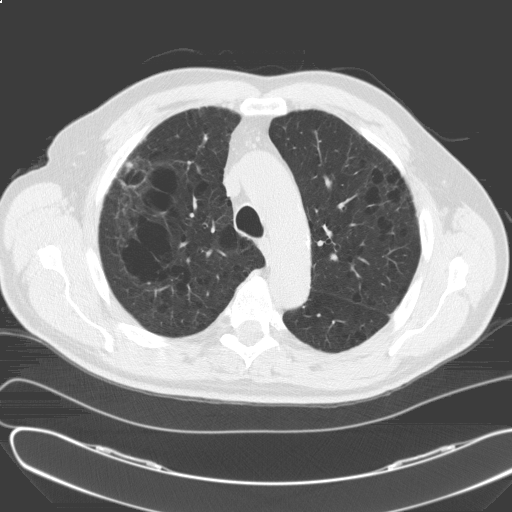
Chest CT (low-dose screening protocol), one axial image. Baseline annual screen. Lung window (W 1500 / L -600 HU). 3.2 mm slice thickness. 512 × 512 image matrix. Male participant, aged 69 years at enrolment.
Lesion marked by an expert reader, bounding box [x1, y1, x2, y2] px = [116, 155, 142, 185]. The screening reader recorded 2 non-calcified nodules or masses ≥4 mm on this exam; which of them this box marks is not recorded. Official screen result: positive, change unspecified: nodule(s) >= 4 mm or enlarging nodule(s), mass(es), or other non-specific abnormalities suspicious for lung cancer.